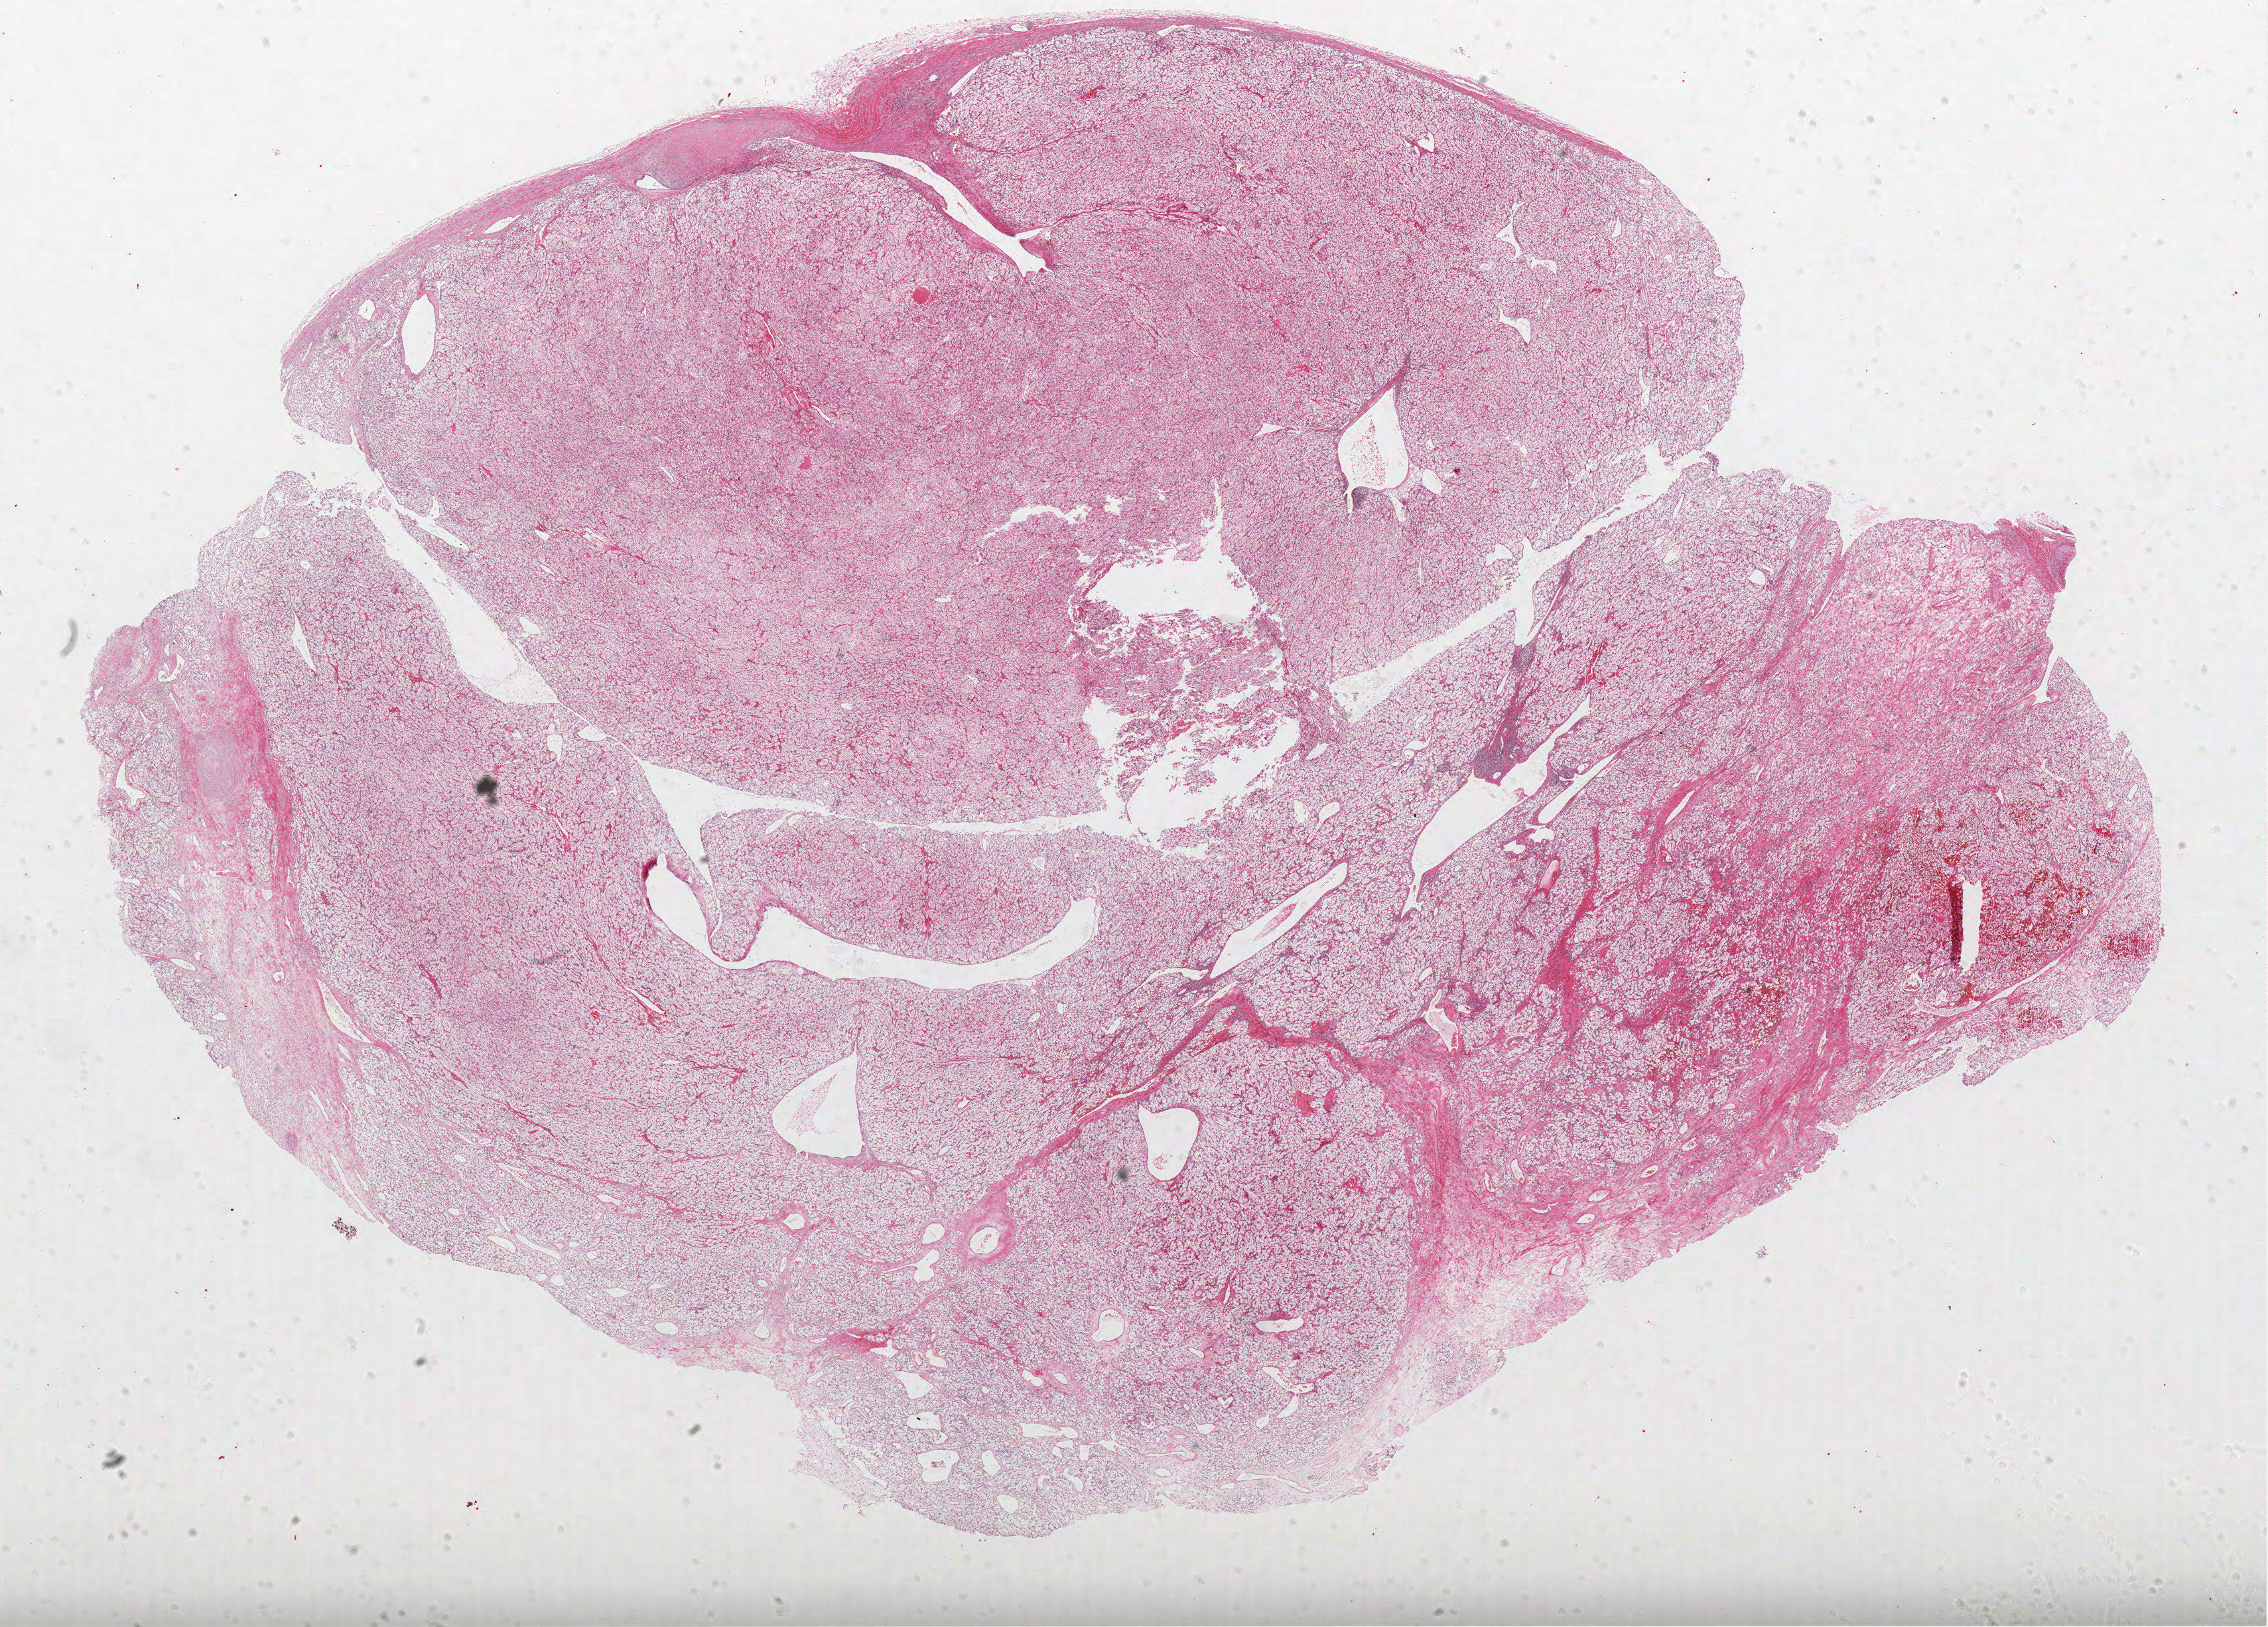
Whole-slide histology image, Hematoxylin and eosin (H&E) stained, shown as a low-resolution overview of the whole scanned area (about 27.3 x 19.6 mm). FFPE section. Kidney, primary tumour sample. Female, age 65 years at initial diagnosis. Histologic grade: G2 (moderately differentiated).
AJCC pathologic stage: I. TNM: T1b N0 M0. Laterality: right. Histologic diagnosis: Clear cell adenocarcinoma, NOS. Lymph nodes positive (case pathology): 0 of 3 examined.